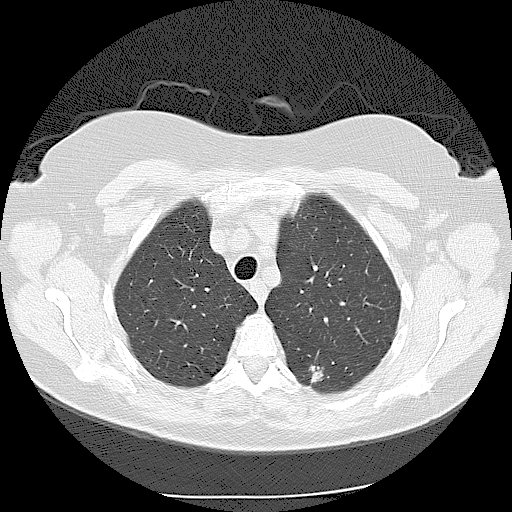
Low-dose screening chest CT, one axial slice; slice 90 of 116 in the series (ordered by position); lung window (W 1500 / L -600 HU); 2.5 mm slice thickness; 512 × 512 image matrix, field of view 360 × 360 mm.
Outlined on this slice (manually delineated by an expert):
- lesion 1 (tumor, lower lobe of left lung): box from (x=309, y=365) to (x=324, y=383) px